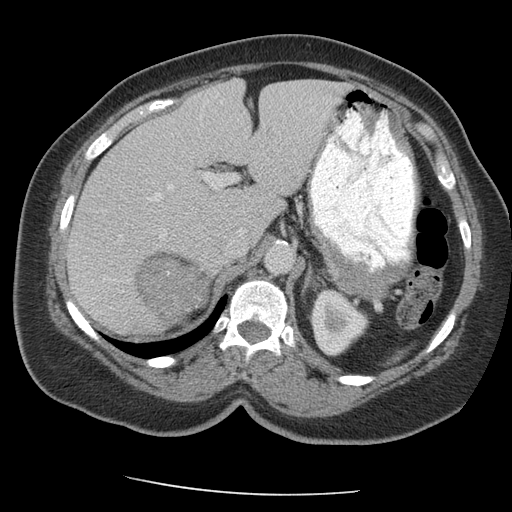
Contrast-enhanced abdominal CT, one axial slice; slice 129 of 163 in the series (ordered by position); 140 kVp; intravenous contrast given; soft-tissue window (W 400 / L 40 HU); 512 × 512 image matrix. Patient: female, 70 years. From the clinical record (not read from this slice): diagnosis: adrenocortical carcinoma; tumour side: right adrenal; tumour size at pathology: 9.5 cm; Ki-67 index: 5 %; stage (as recorded): 2.
Outlined on this slice (semi-automatic segmentation, software-assisted and operator-edited):
- mass: bounding box <137,256,211,323> (left, top, right, bottom; pixels)